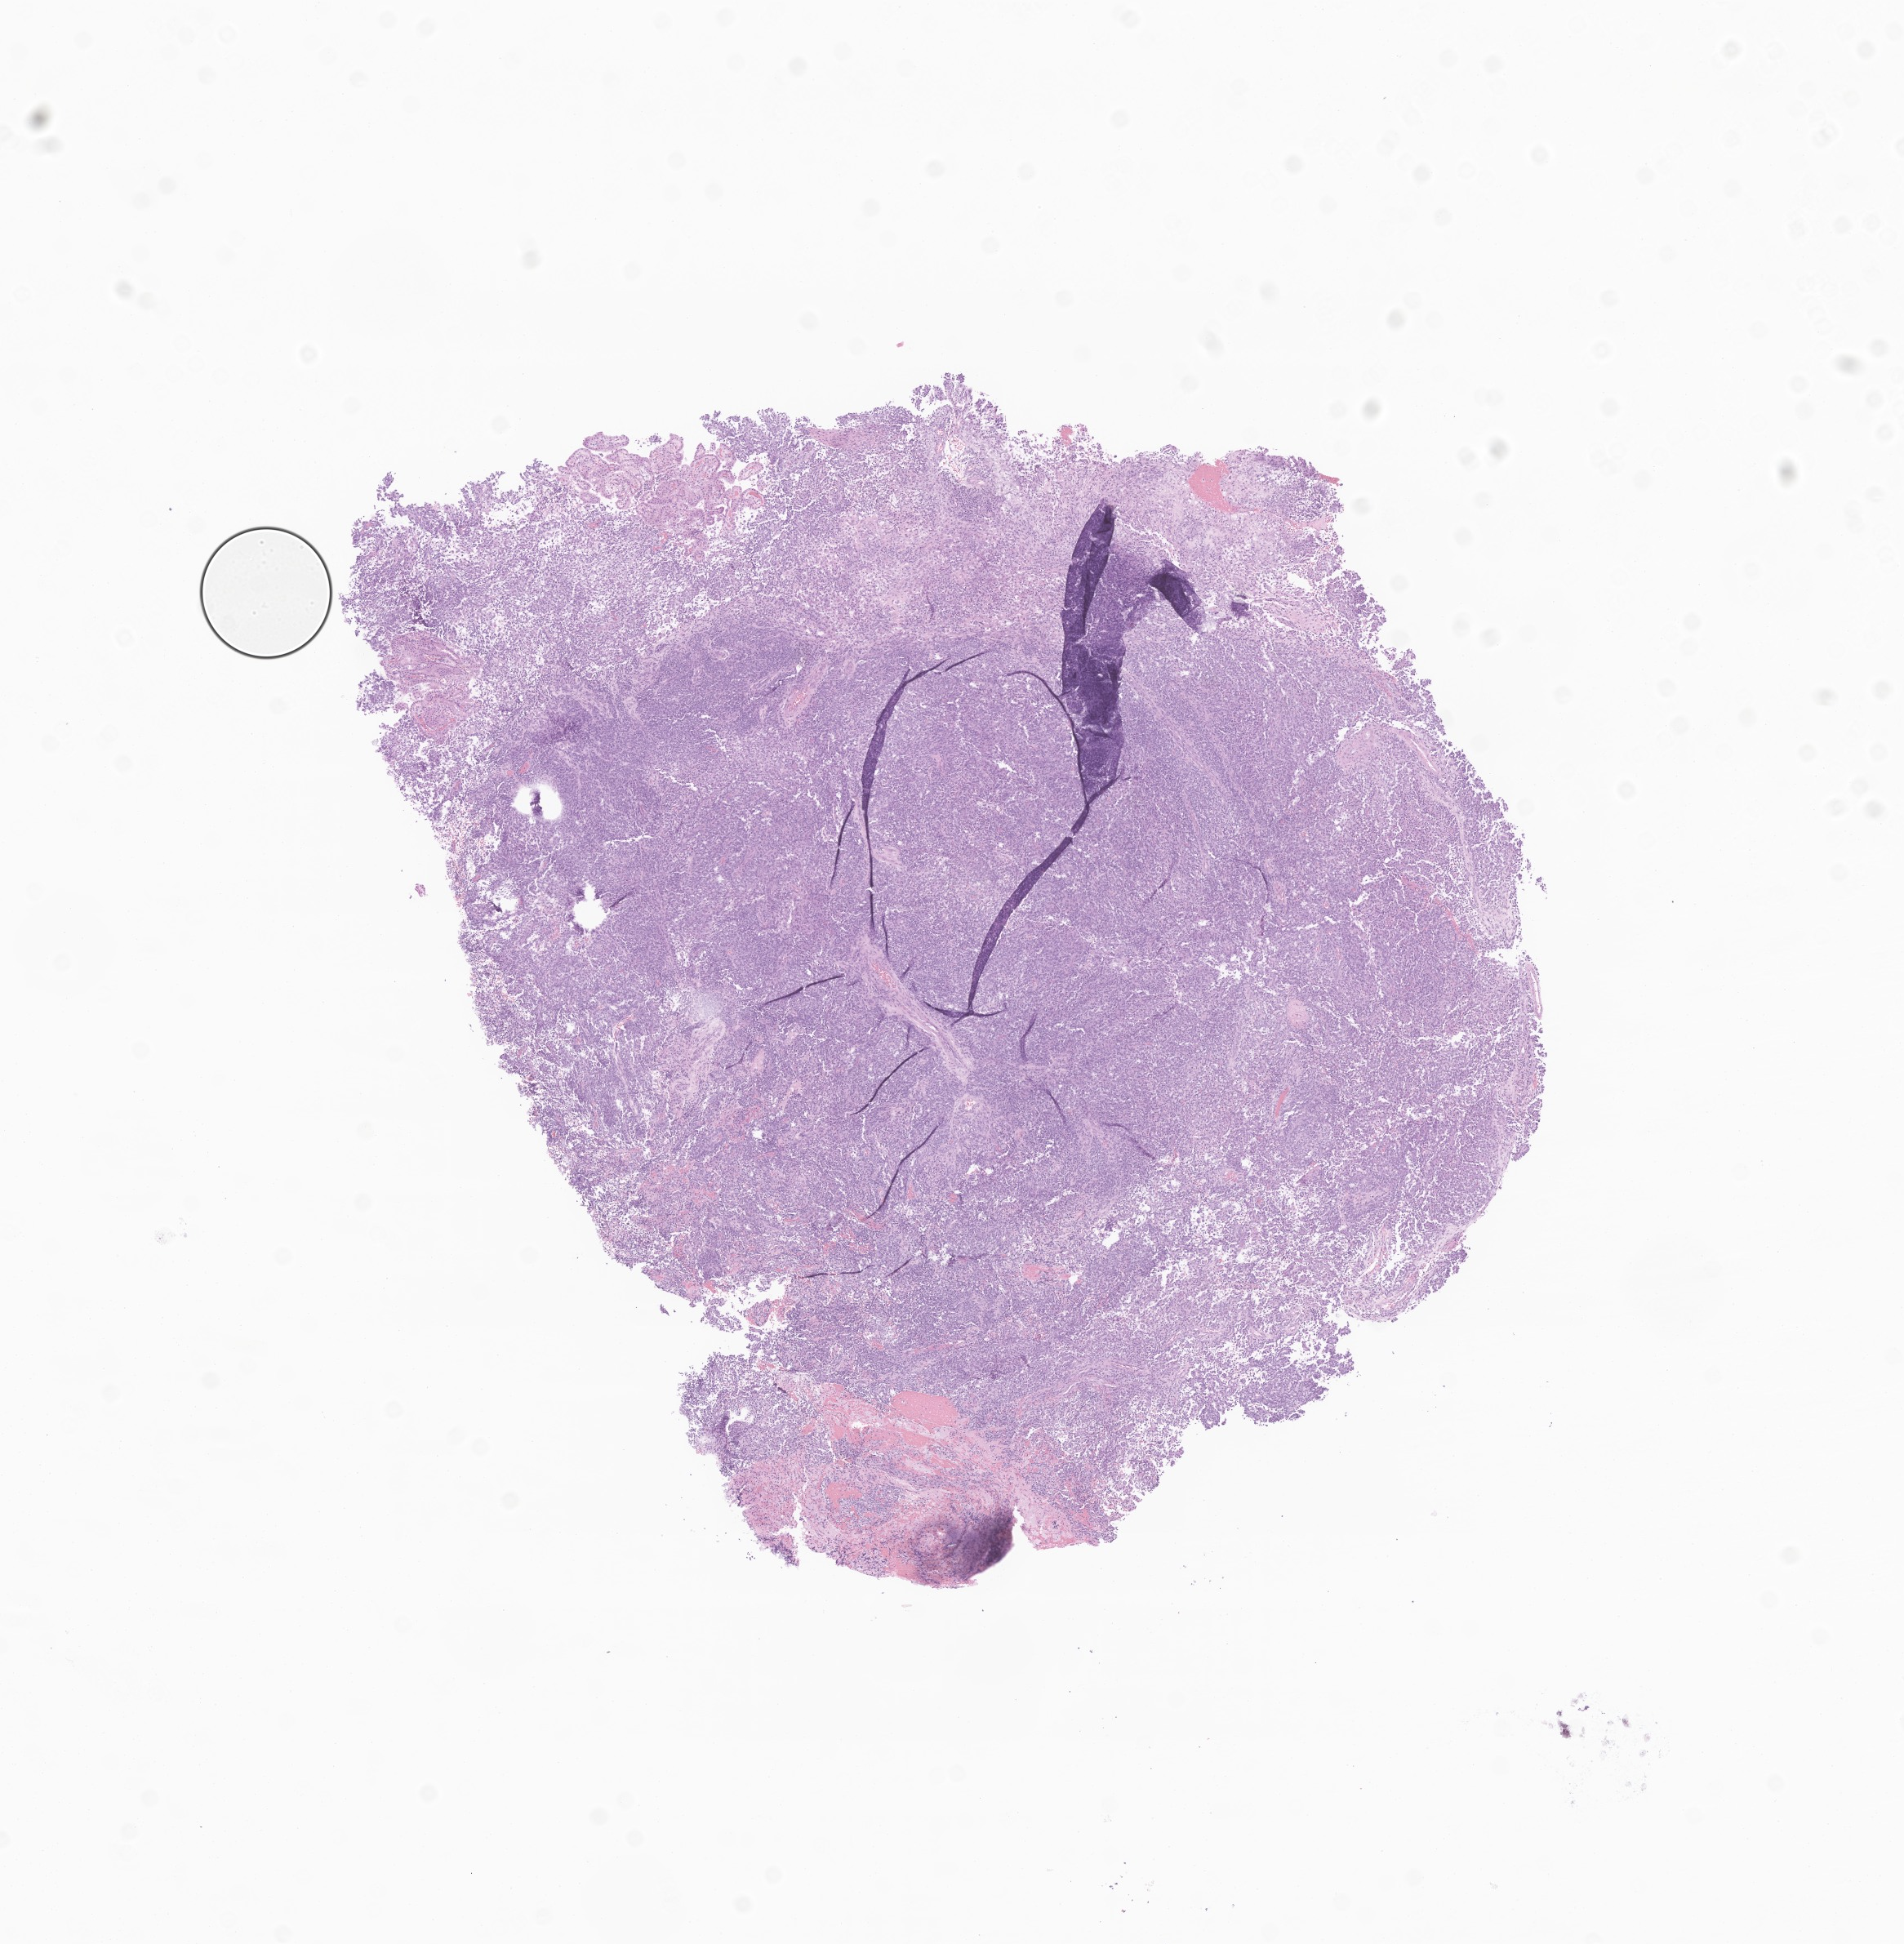
Haematoxylin and eosin whole-slide image of tumor tissue from the cerebellum, shown as a low-resolution overview of the whole scanned area (about 9.8 x 10.0 mm); formalin-fixed, paraffin-embedded (FFPE) tissue. Patient: female, age 406 days (about 1.1 years).
Diagnosis: Atypical teratoid/rhabdoid tumor.